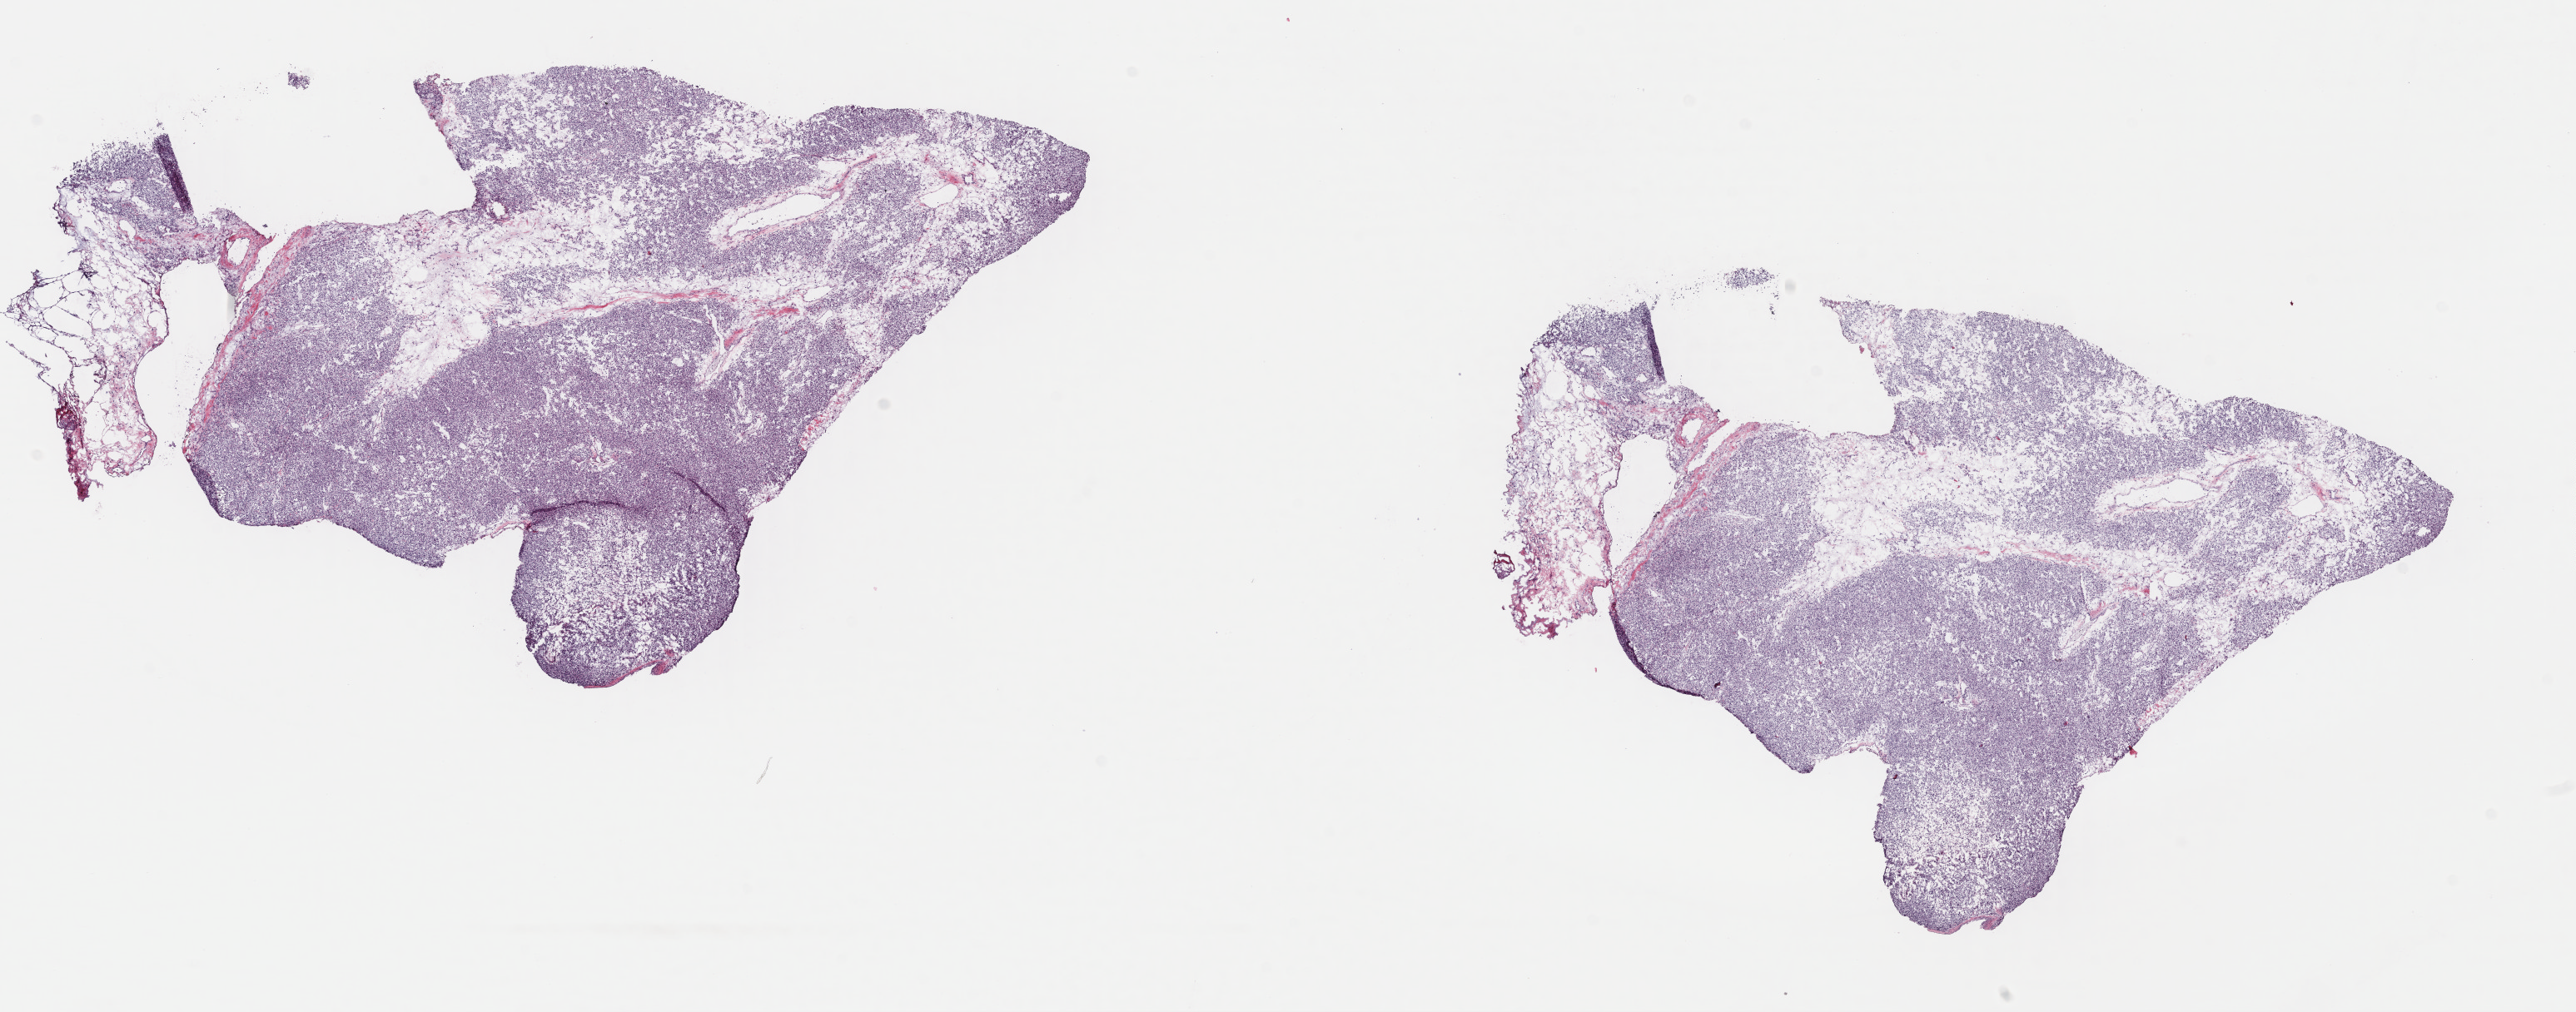
Whole-slide histology image, H&E-stained — low-resolution overview of the scanned area, about 24.3 x 9.6 mm (acquisition: 40x scan); frozen section; kidney, primary tumour sample. Patient: female, age at initial diagnosis 76 years. Slide review estimates, as recorded: tumour cells 80%, tumour nuclei 80%, normal cells 0%, stromal cells 19%, necrosis 1%. Inflammatory infiltration, as recorded: lymphocyte infiltration 4%, monocyte infiltration 2%, neutrophil infiltration 2%.
• histologic diagnosis: Renal cell carcinoma, NOS
• AJCC pathologic stage: I (7th edition)
• laterality: right